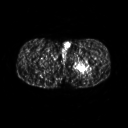
FDG PET of an extremity soft-tissue mass (from a PET/CT study), one axial slice. Slice 251 of 267 in the series (ordered by position). 128 × 128 image matrix, field of view 500 × 500 mm. Male patient, age 27 years. Case-level facts recorded for this patient, not image findings: histological type: extraskeletal osteosarcoma; grade: high; site of the primary tumour: left adductur.
Structures marked on this image (expert contour drawn on MRI and transferred to this co-registered scan by the dataset authors):
- gross tumour volume (mass): bounding box [x1, y1, x2, y2] px = [72, 56, 95, 74]